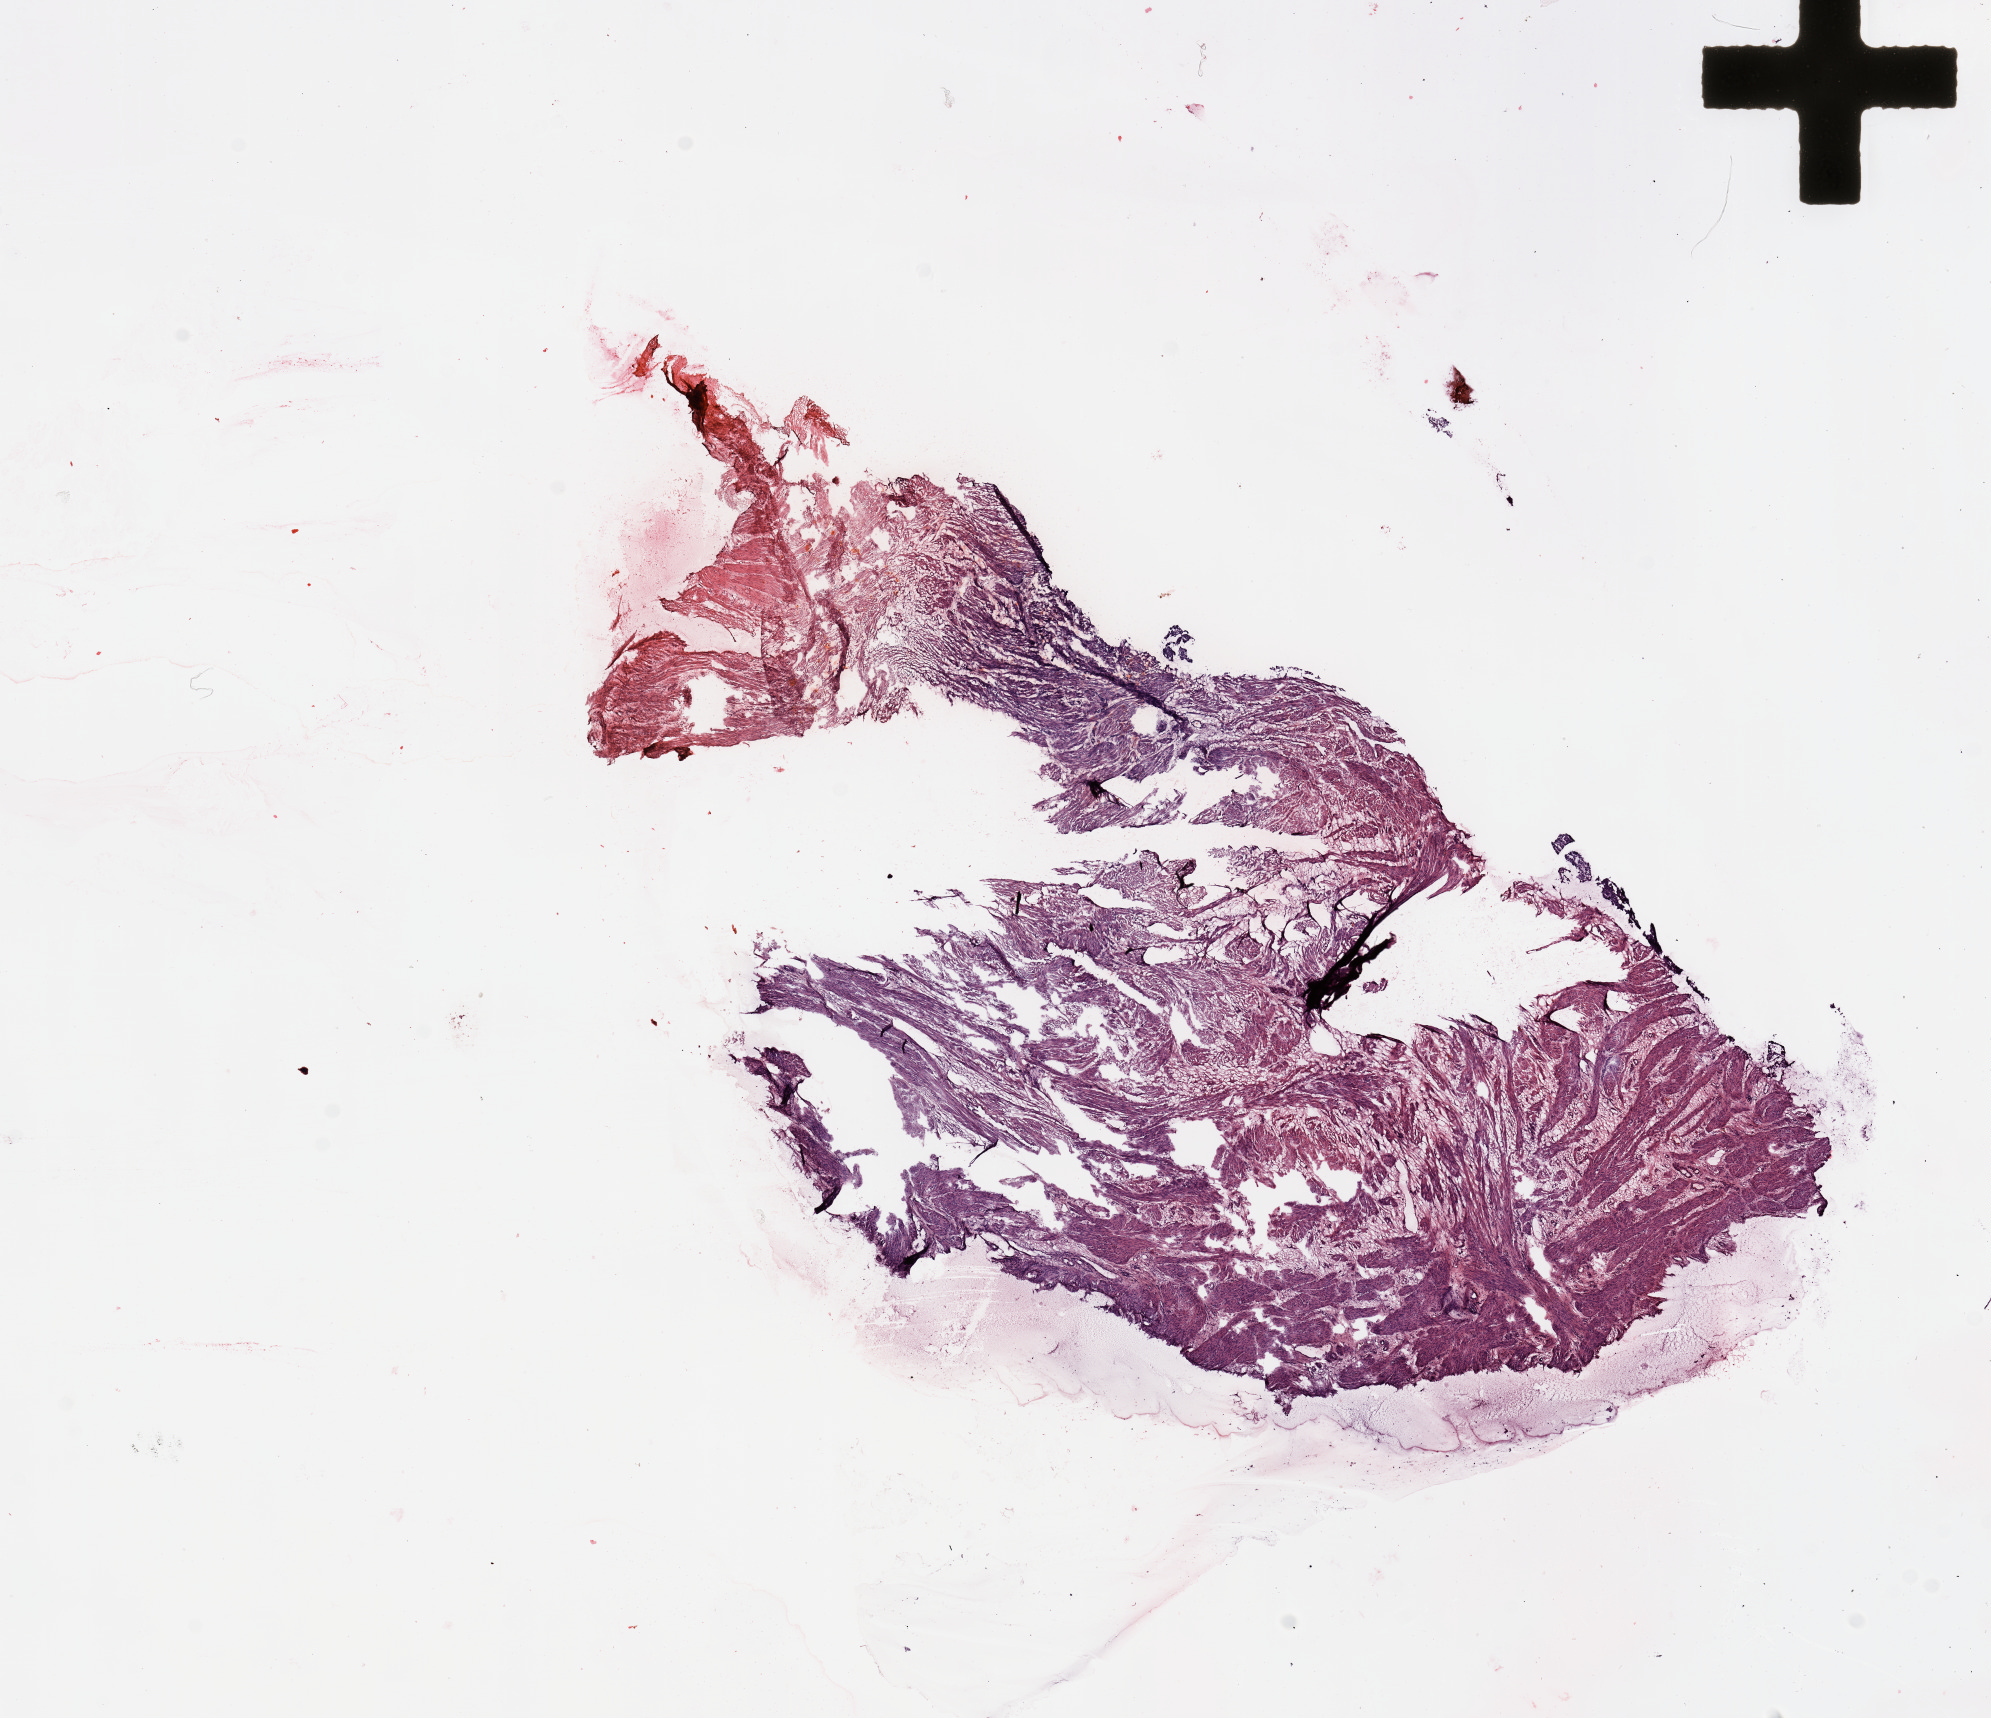
H&E-stained whole-slide image, a low-resolution overview of the entire scanned area, about 15.8 x 13.6 mm (acquisition: 20x scan); uterus, normal (non-tumour) tissue. 45-year-old female patient.
This section: normal (non-tumour) tissue from the same patient. Patient diagnosis: Endometrioid adenocarcinoma, NOS.